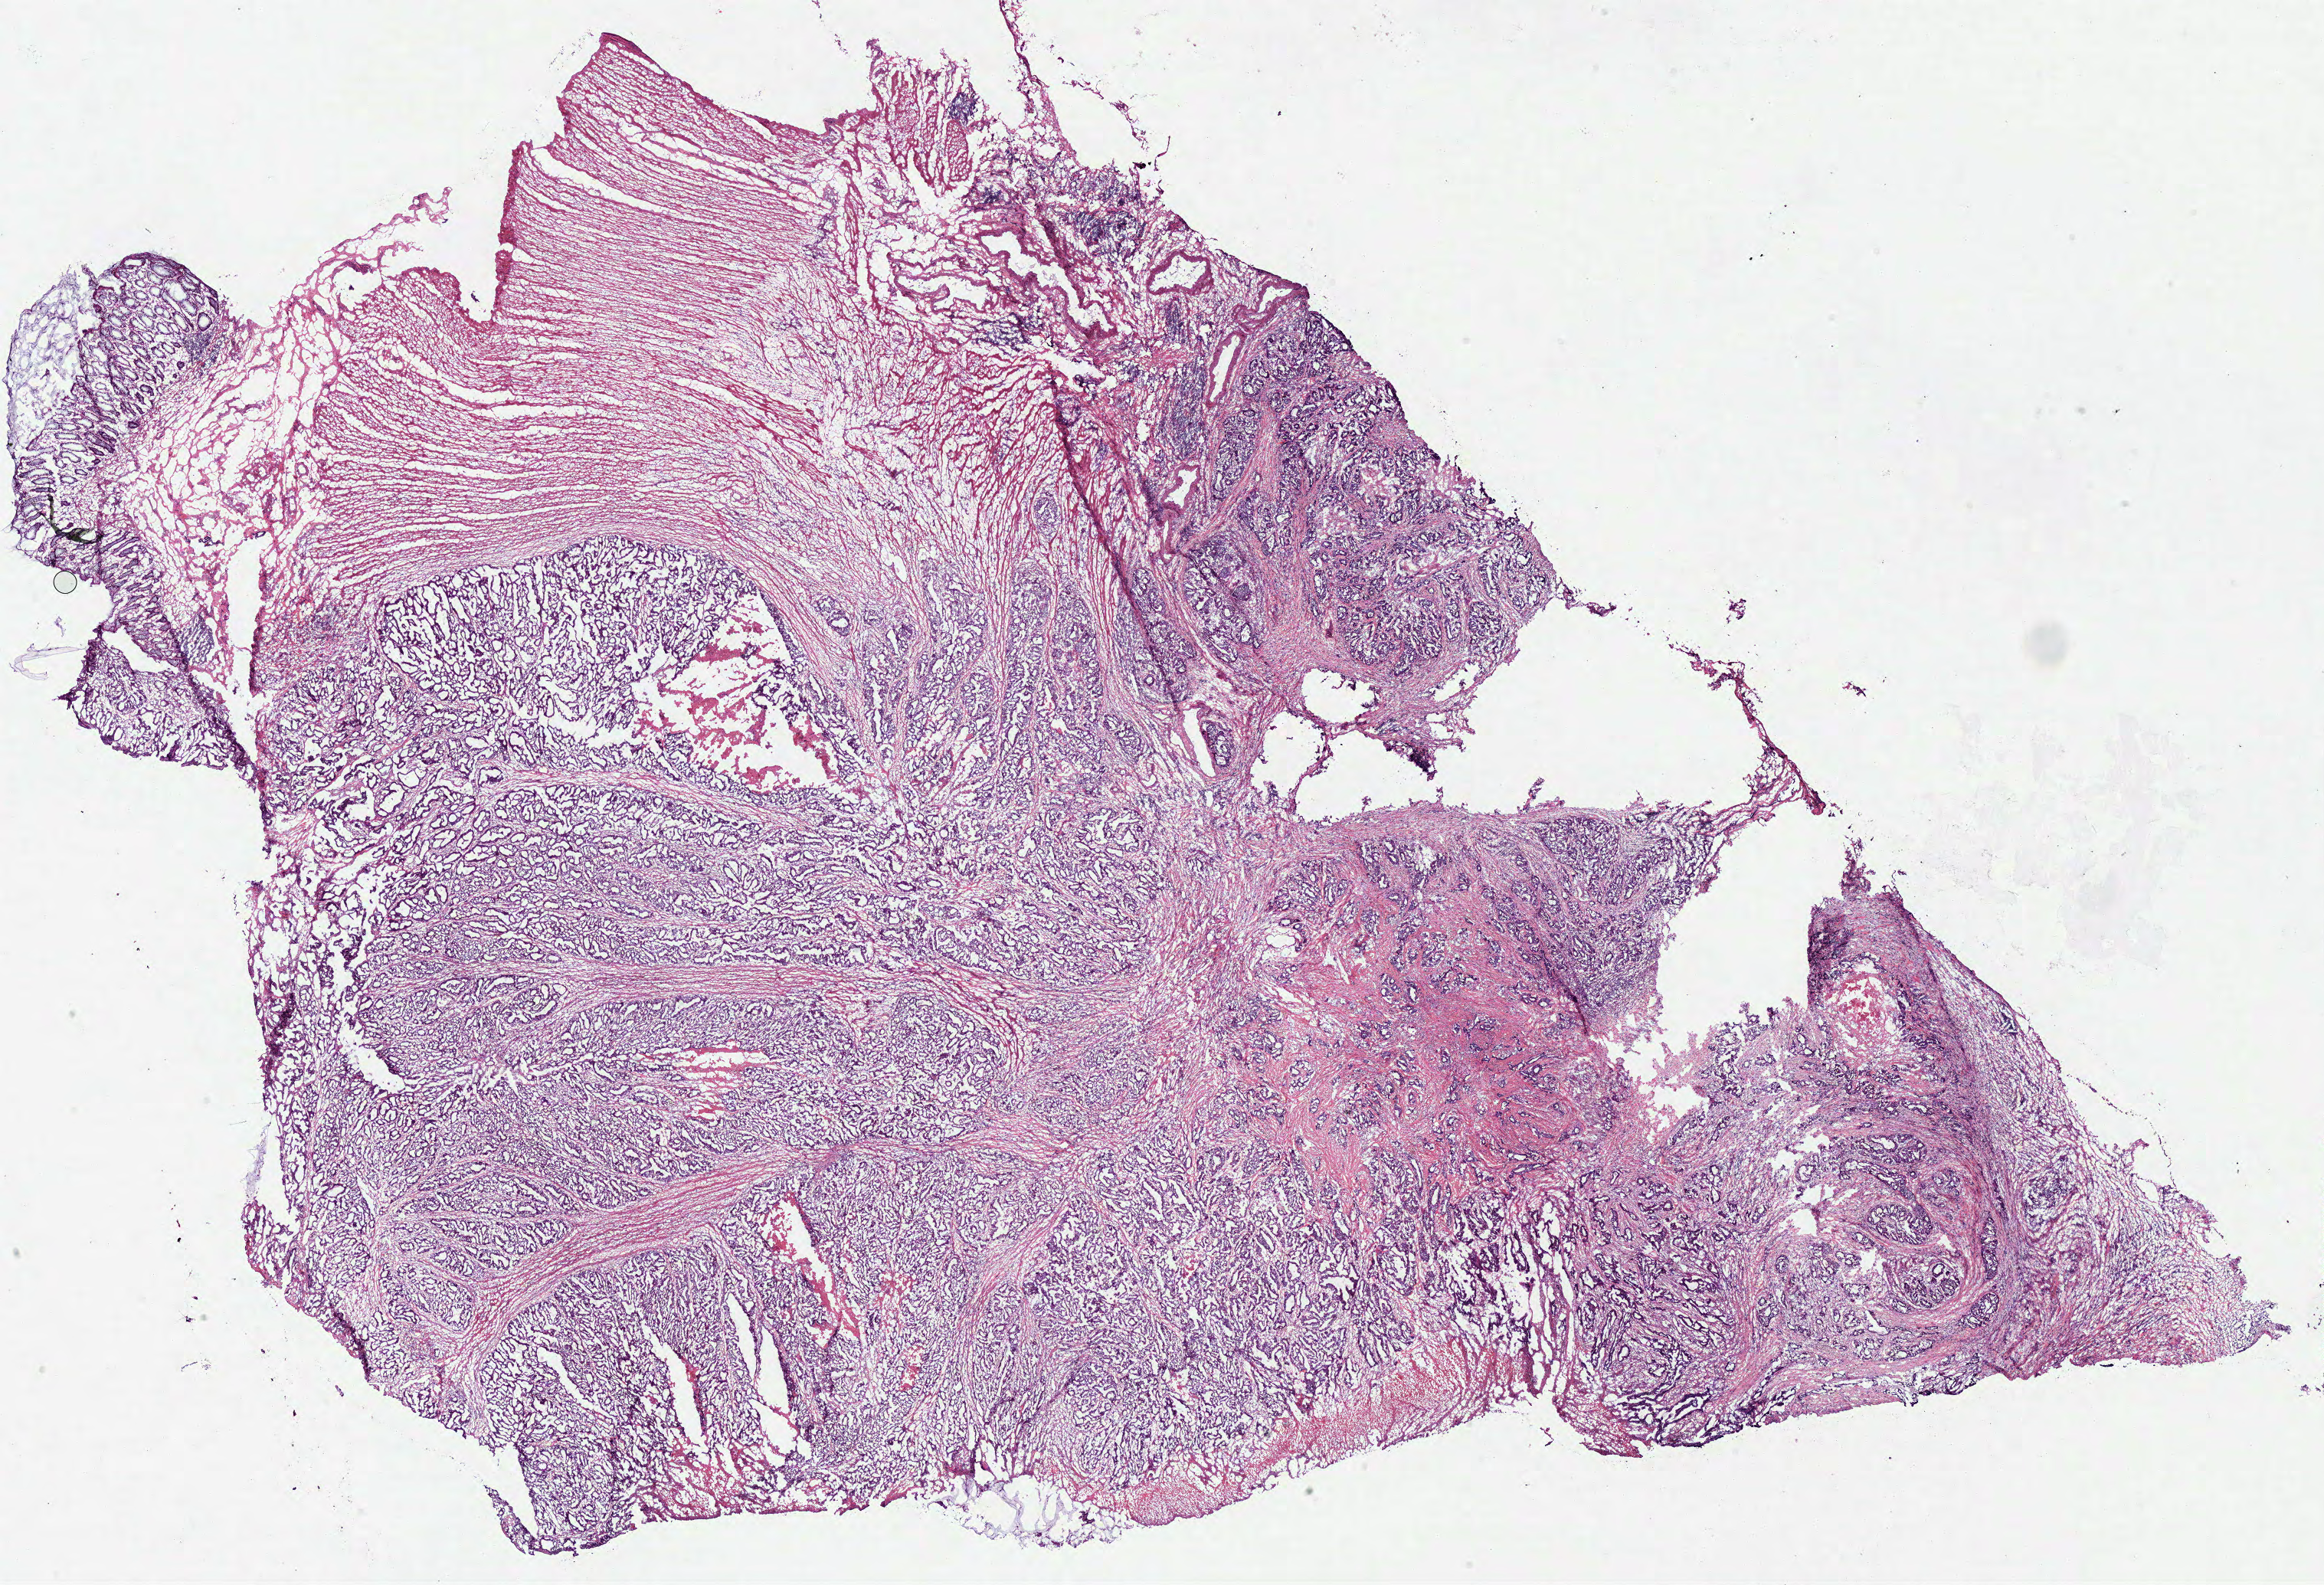
Whole-slide histology image, H&E, low-resolution overview of the scanned area, about 23.9 x 16.3 mm (slide scanned at 40x). Frozen section from the top of the tissue portion. Sample: primary tumour, rectum. Patient: male, age at initial diagnosis 70 years. Slide review estimates, as recorded: tumour cells 80%, tumour nuclei 80%, normal cells 15%, necrosis 5%. Inflammatory infiltration, as recorded: lymphocyte infiltration 10%, monocyte infiltration 5%.
Pathologic diagnosis: Adenocarcinoma, NOS (connective, subcutaneous and other soft tissues of abdomen). AJCC pathologic stage: IIIC. TNM: T4a N2 M0.